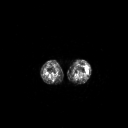
FDG PET of an extremity soft-tissue mass (from a PET/CT study), one axial slice. Position 166 of 223 along the scan axis. 3.27 mm slice thickness. 128 × 128 image matrix, field of view 700 × 700 mm. Female patient, age 16 years. From the clinical record (not read from this slice): histological type: spindle cell suggestive of biphasic synovial sarcoma; grade: intermediate; site of the primary tumour: left knee.
Structures marked on this image (expert contour drawn on MRI and transferred to this co-registered scan by the dataset authors):
- gross tumour volume including surrounding oedema: box from (x=85, y=67) to (x=88, y=73) px
- gross tumour volume (mass): (x=85, y=67)–(x=88, y=73)